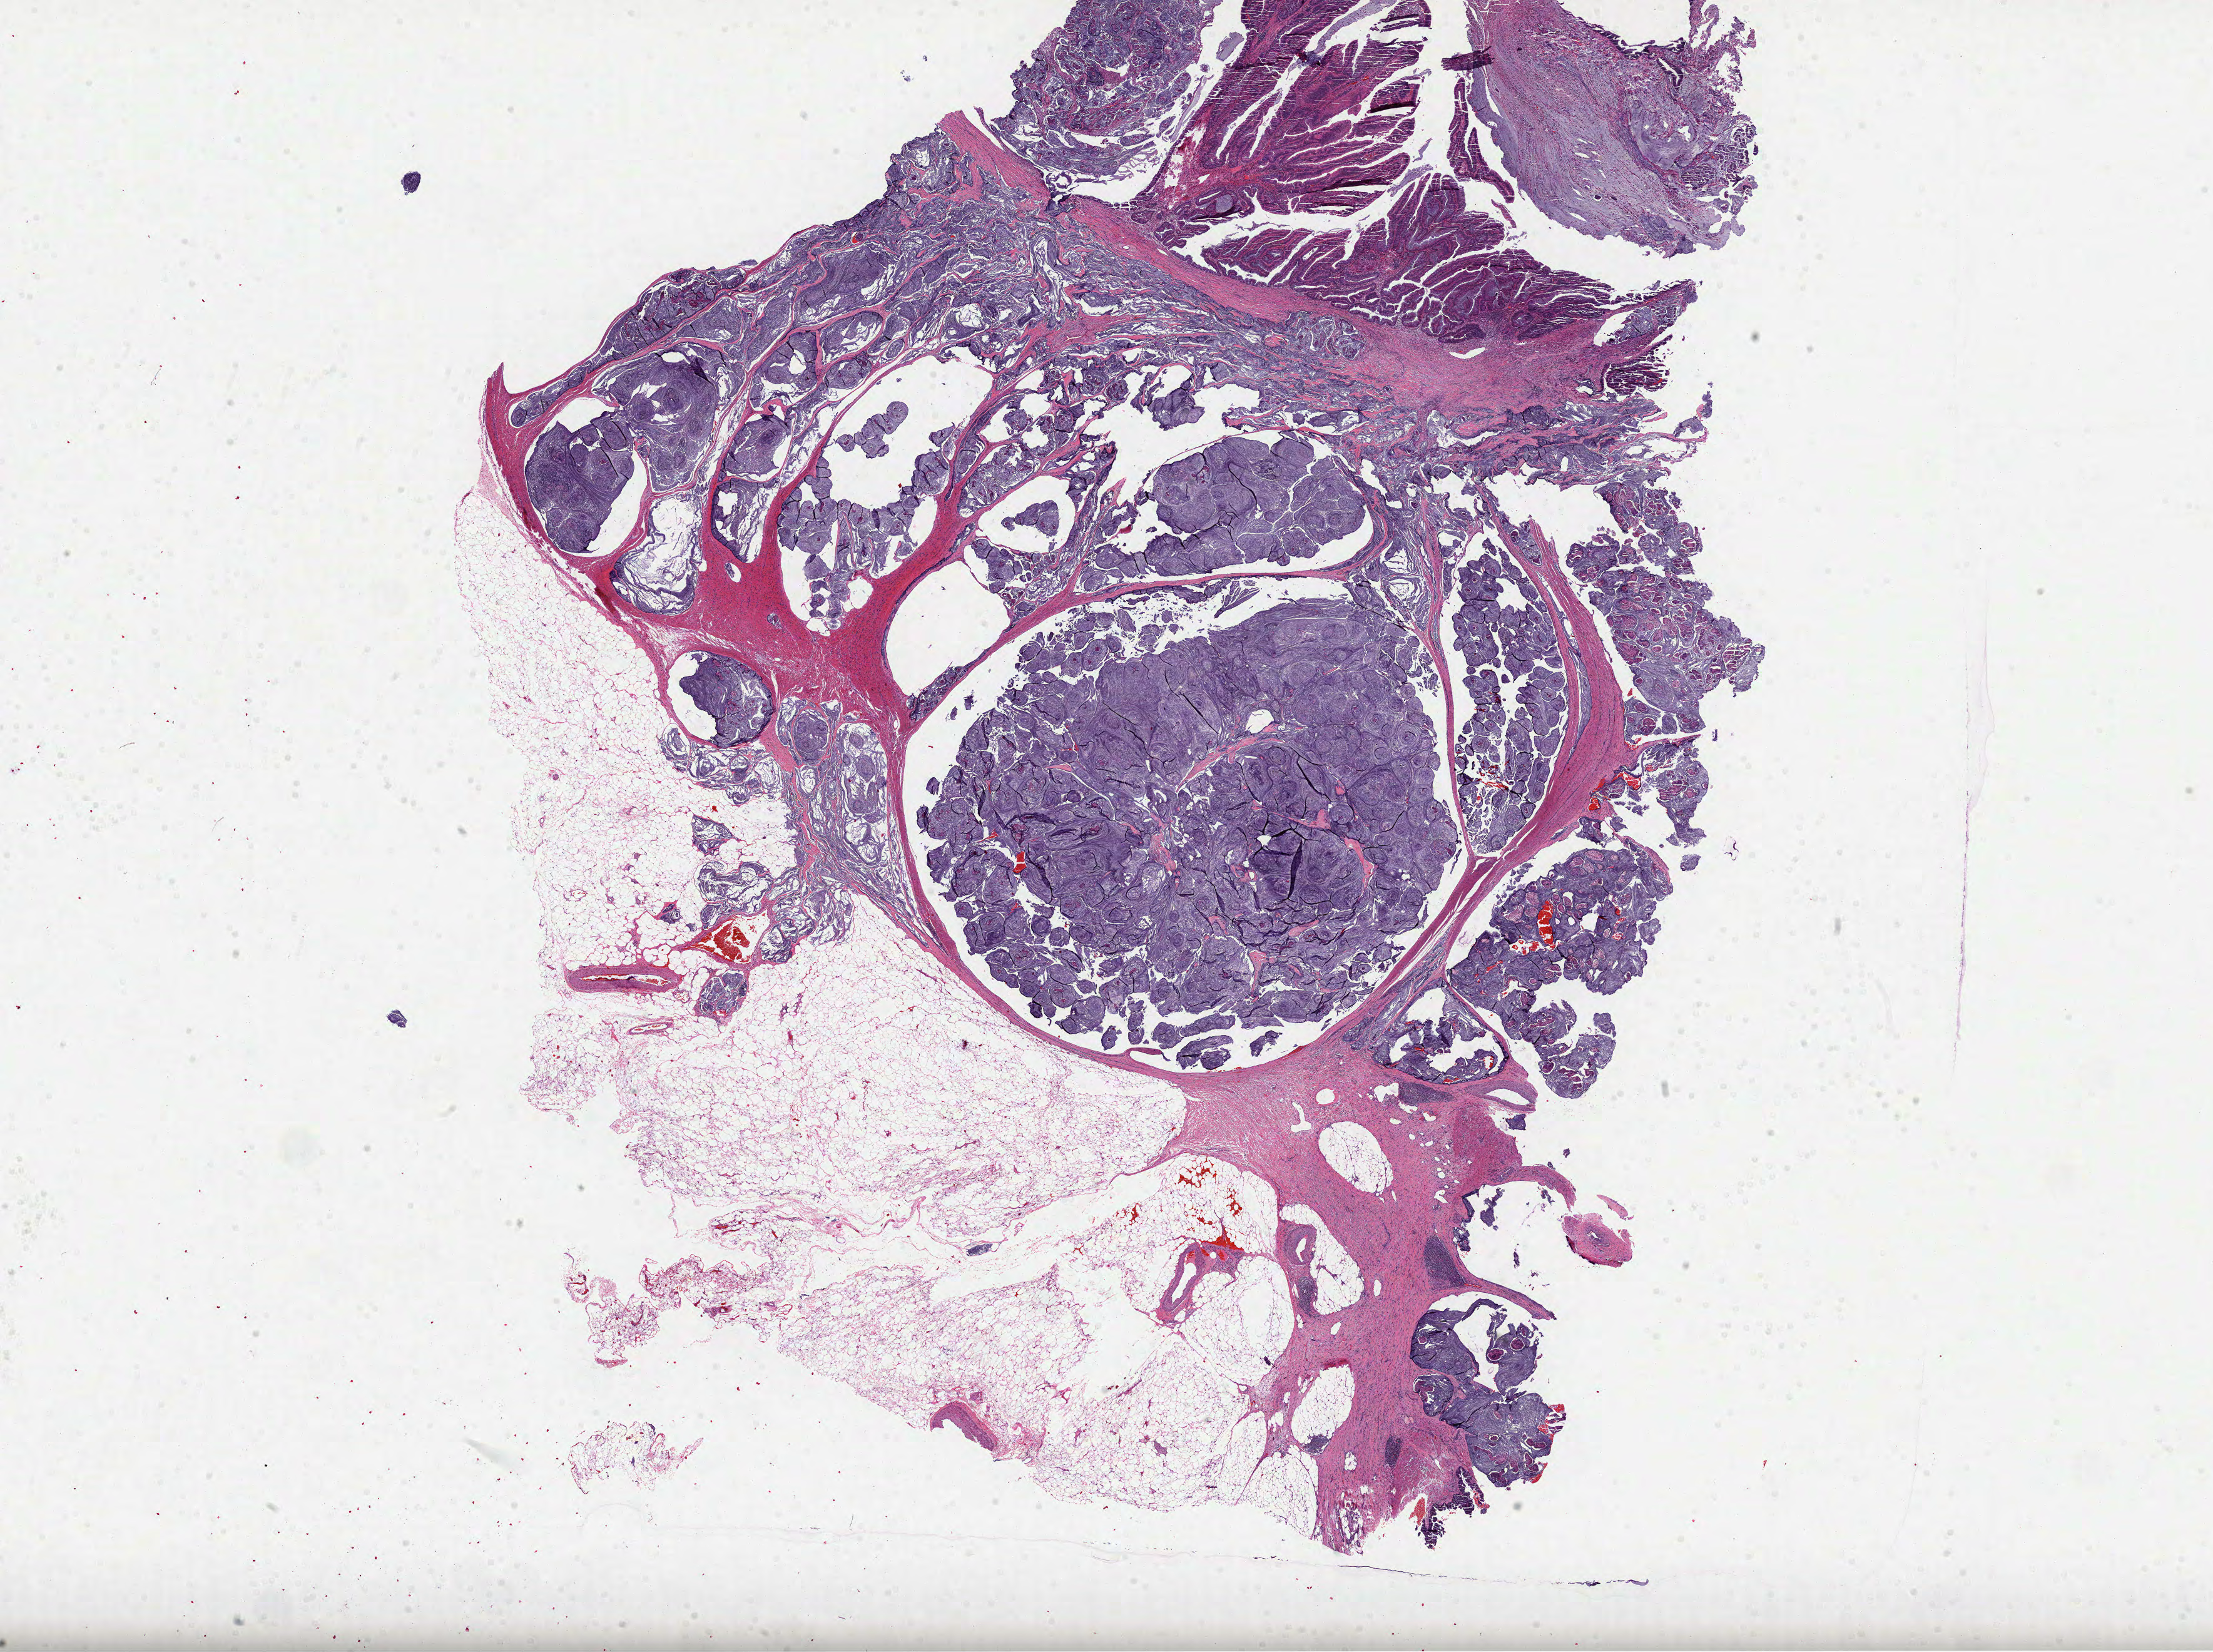
Whole-slide histology image, H&E — low-resolution overview of the scanned area, about 28.5 x 21.3 mm. Formalin-fixed paraffin-embedded (FFPE) diagnostic section. Colon, primary tumour sample. Female, age 60 years at initial diagnosis.
• diagnosis: Mucinous adenocarcinoma
• AJCC pathologic stage: IIIB (7th edition)